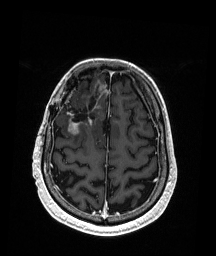
Brain MRI from a brain-tumour surgery series, one axial slice. Slice 52 of 192 in the series (ordered by position). T1-weighted post-contrast. 1 mm slice thickness. 216 × 256 image matrix, field of view 211 × 250 mm. Case-level facts recorded for this patient, not image findings: histopathology: Astrocytoma; WHO grade: 3; IDH mutation: yes; tumour location: Right Frontal.
Structures marked on this image (manually delineated by an expert):
- previous resection cavity: bounding box <65,93,99,122> (left, top, right, bottom; pixels)
- tumour: <68,85,108,135>